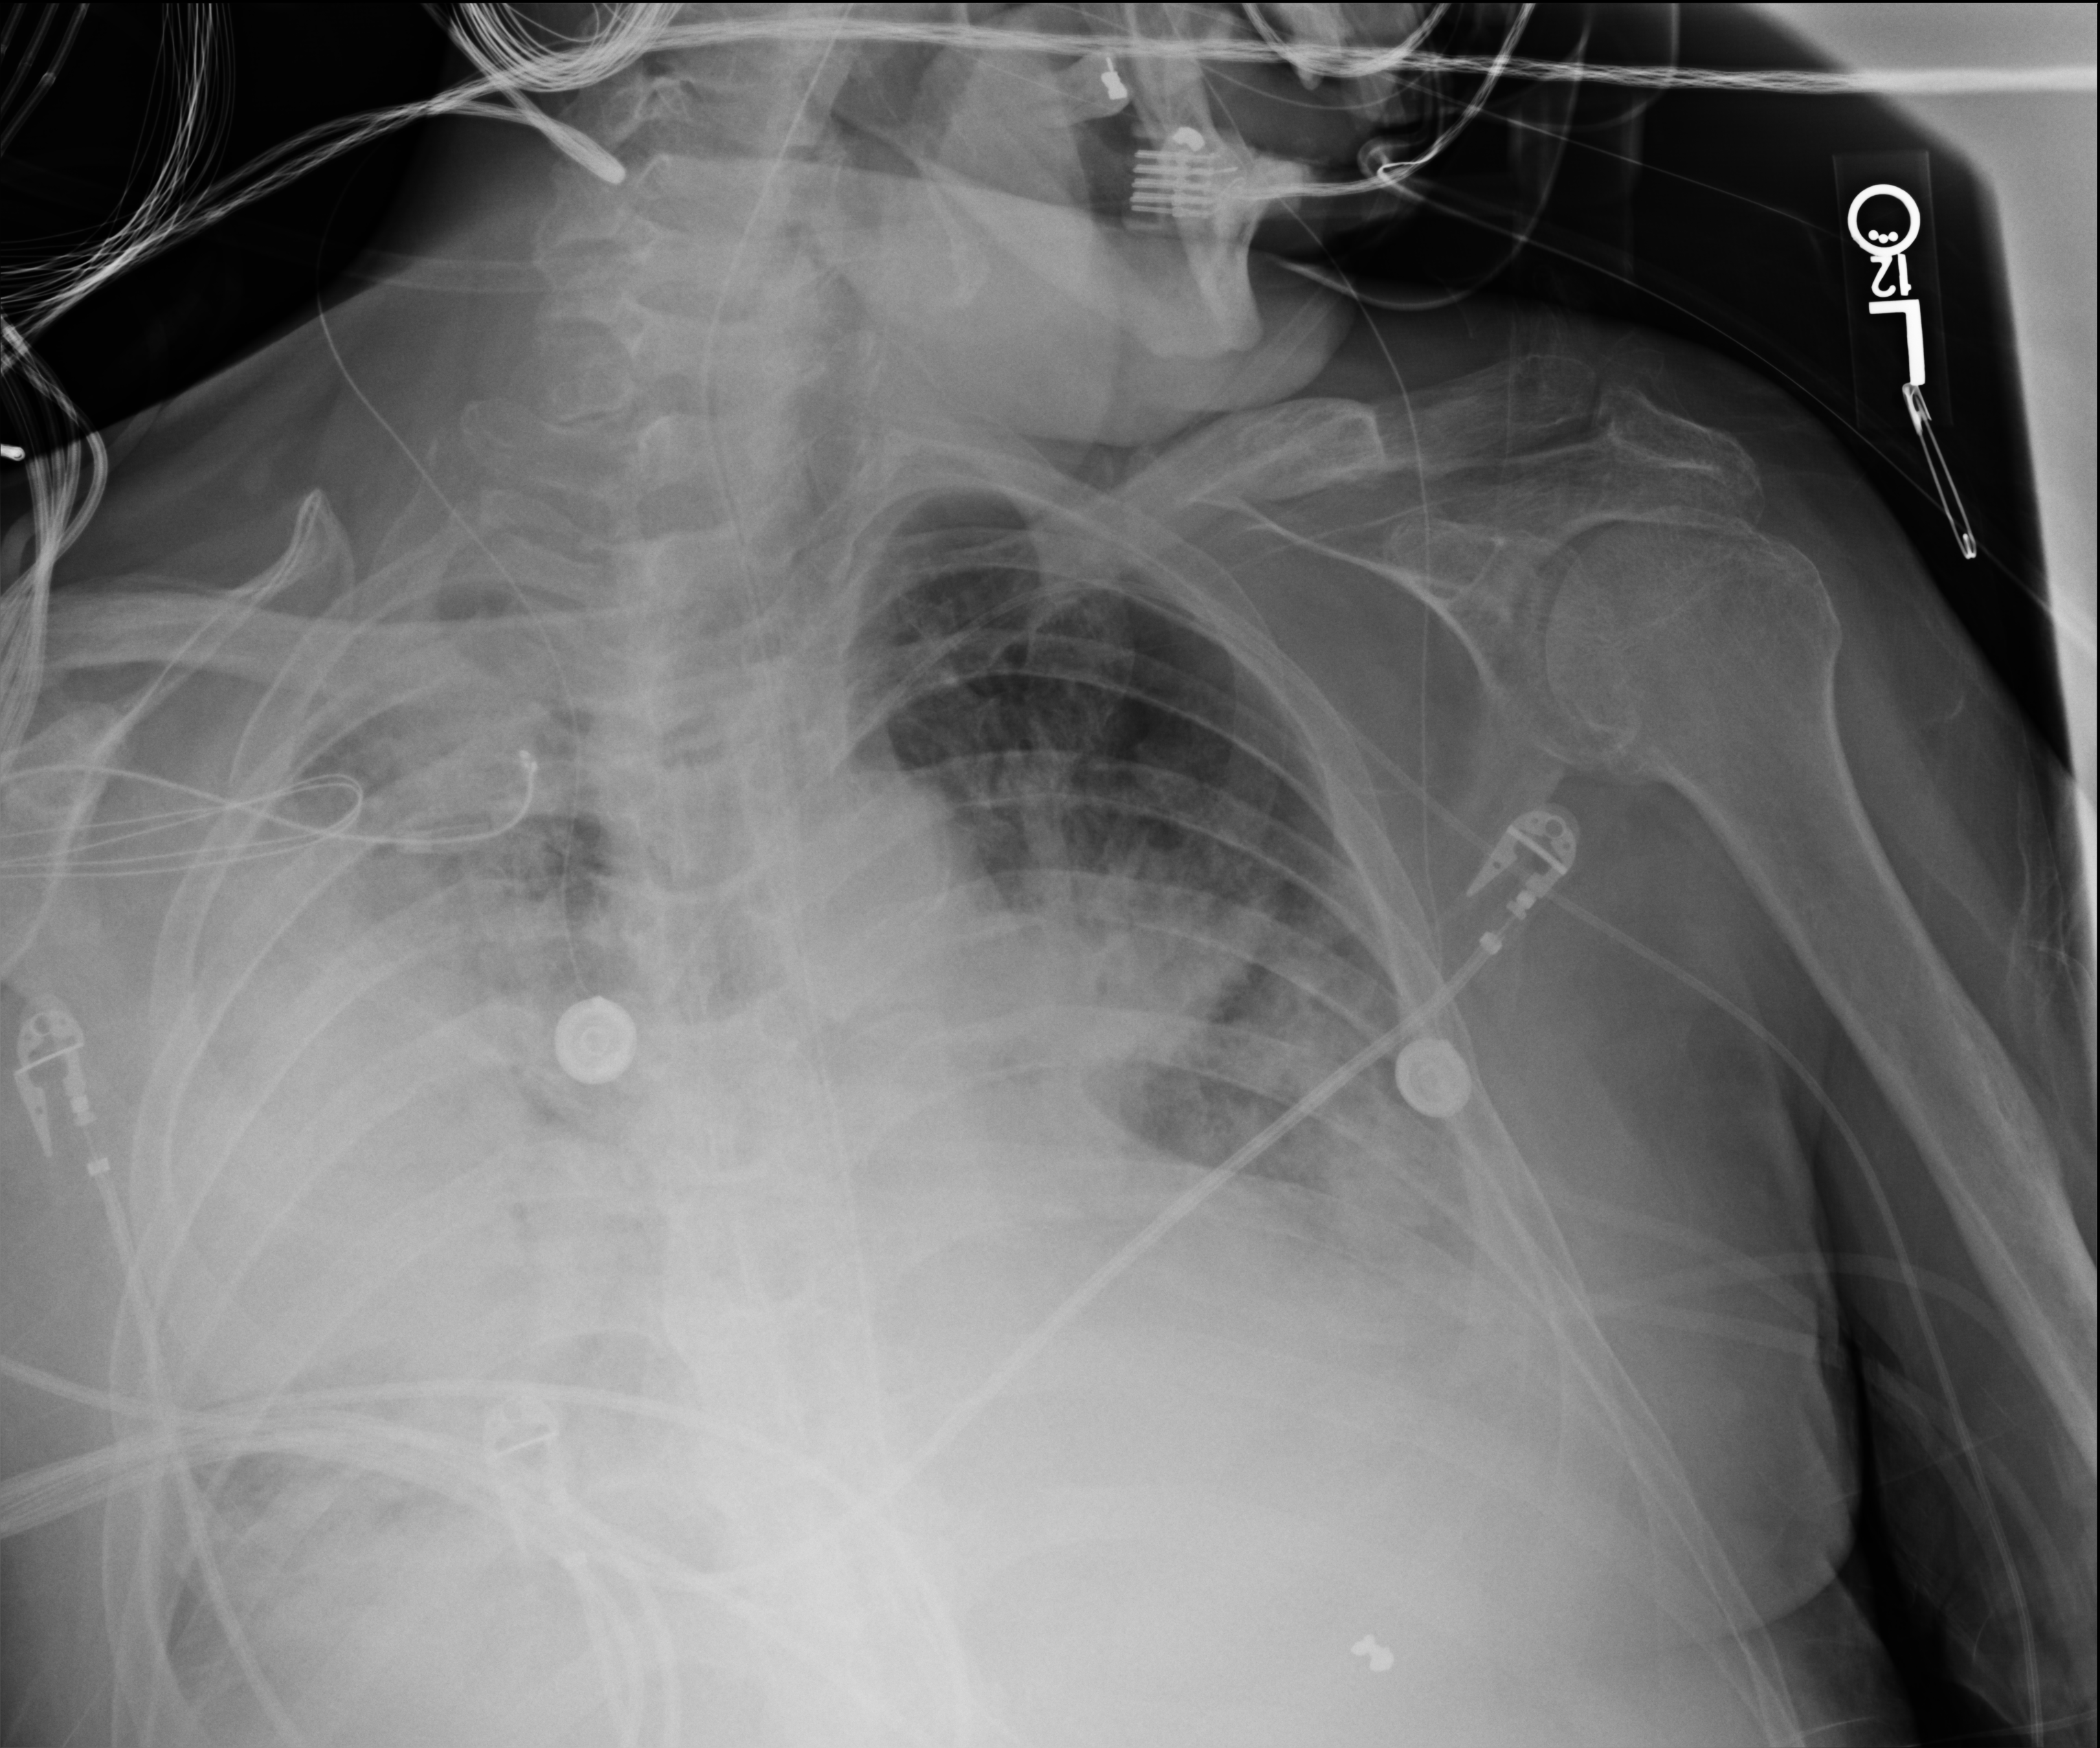
Bedside chest radiograph (computed radiography). Male patient hospitalised with COVID-19, age 60–74 years.
Hospital-stay facts (about this admission, not read from this image; timing relative to this image not recorded):
- mechanically ventilated during this hospital stay: no